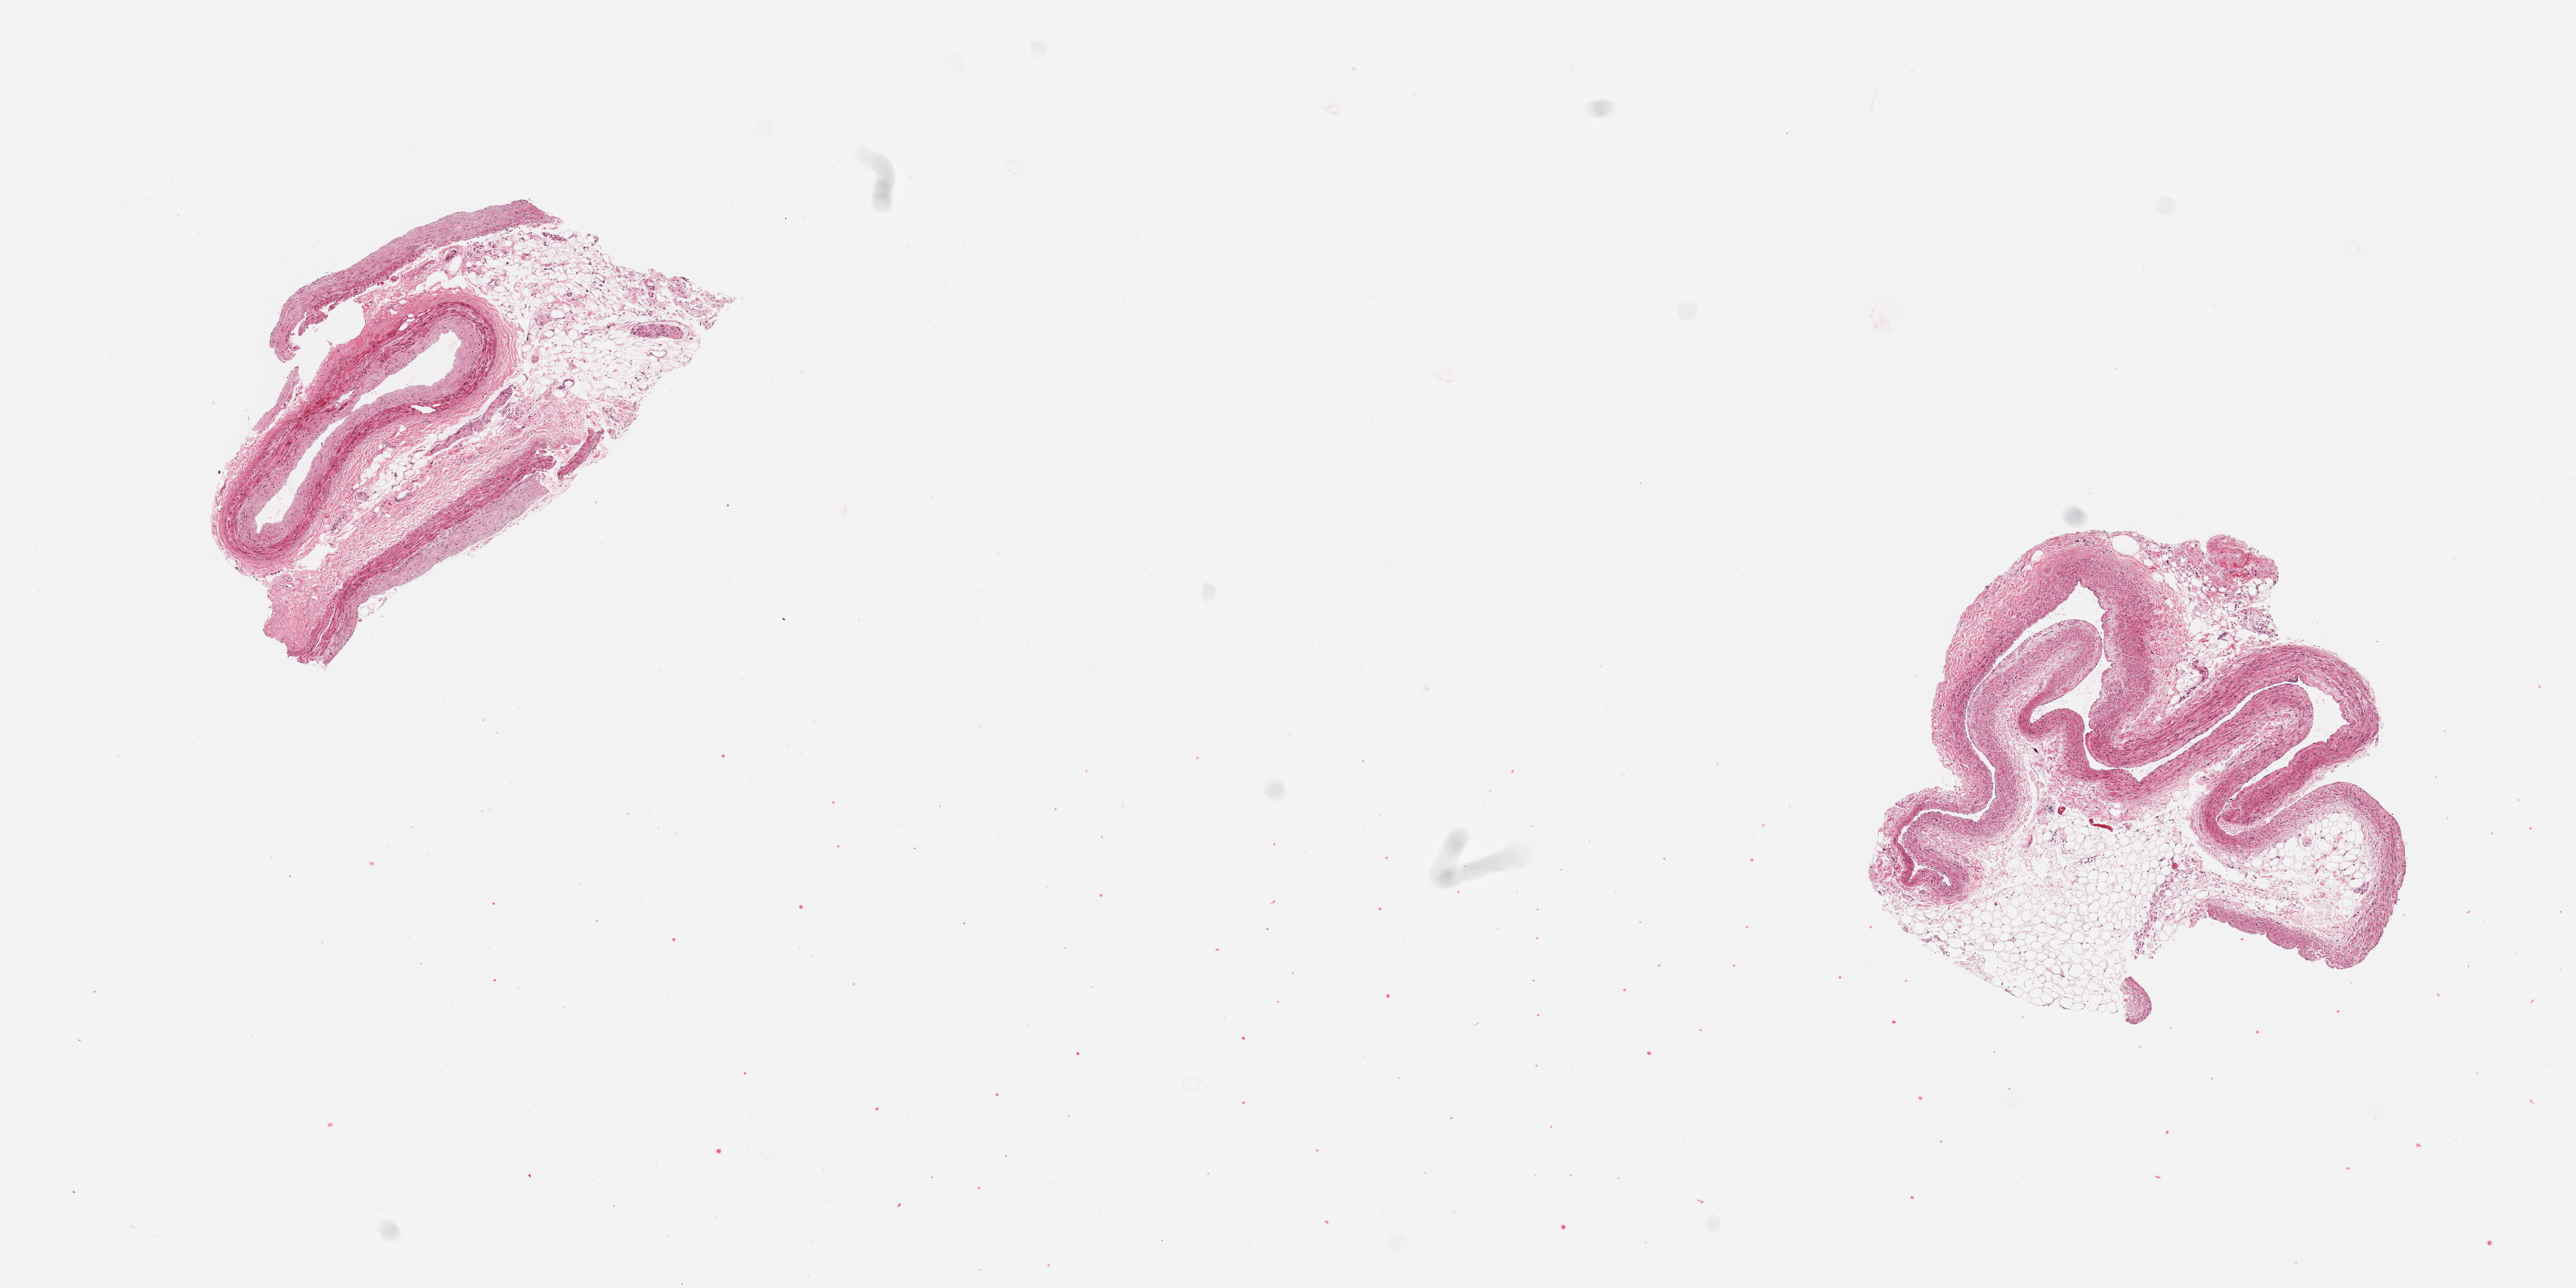
Digitized hematoxylin and eosin (H&E)-stained section — low-resolution overview of the scanned area, about 14.8 x 7.4 mm (from a 20x scan), PAXgene-fixed, paraffin-embedded tissue, target tissue: coronary artery, donor tissue sample. Male donor.
Pathologist's review note for this sample: 2 pieces; one artery, one vein.